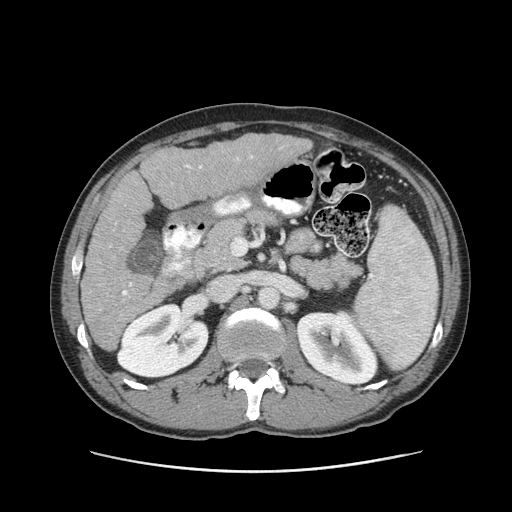
Contrast-enhanced abdominal CT (liver protocol), one axial slice. Position 43 of 93 along the scan axis. Soft-tissue window (W 400 / L 40 HU). 512 × 512 image matrix, field of view 380 × 380 mm. From the clinical record (not read from this slice): diagnosis: hepatocellular carcinoma (patient treated with transarterial chemoembolisation; whether this scan precedes or follows treatment is not stated here); TNM stage (as recorded): Stage-II.
Structures marked on this image (semi-automatically segmented with operator editing):
- liver parenchyma outside the tumour (the mass and vessels are separate outlines, so this box may not span the whole liver): bounding box (x1, y1, x2, y2) in pixels: (82, 134, 312, 350)
- liver vessels: (122, 156, 253, 295)